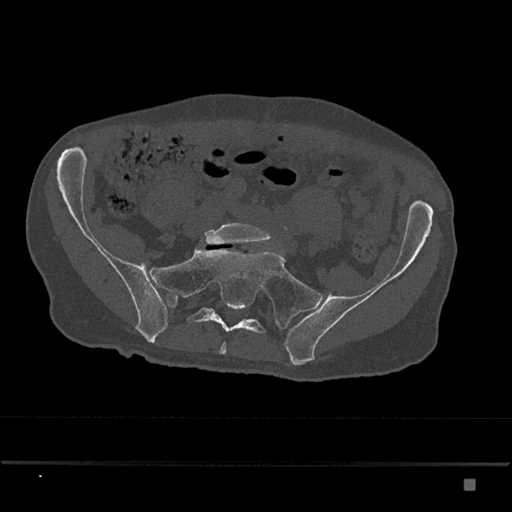
CT including the spine, one axial slice; slice 219 of 797 in the series (ordered by position); reconstruction kernel Br40s/3; 120 kVp; bone window (W 1800 / L 400 HU); 512 × 512 image matrix, field of view 390 × 390 mm. Patient: male, 72 years. From the clinical record (not read from this slice): primary cancer: prostate.
Outlined on this slice (semi-automatic segmentation, software-assisted and operator-edited):
- L5 vertebra: bounding box (x1, y1, x2, y2) in pixels: (204, 223, 272, 245)